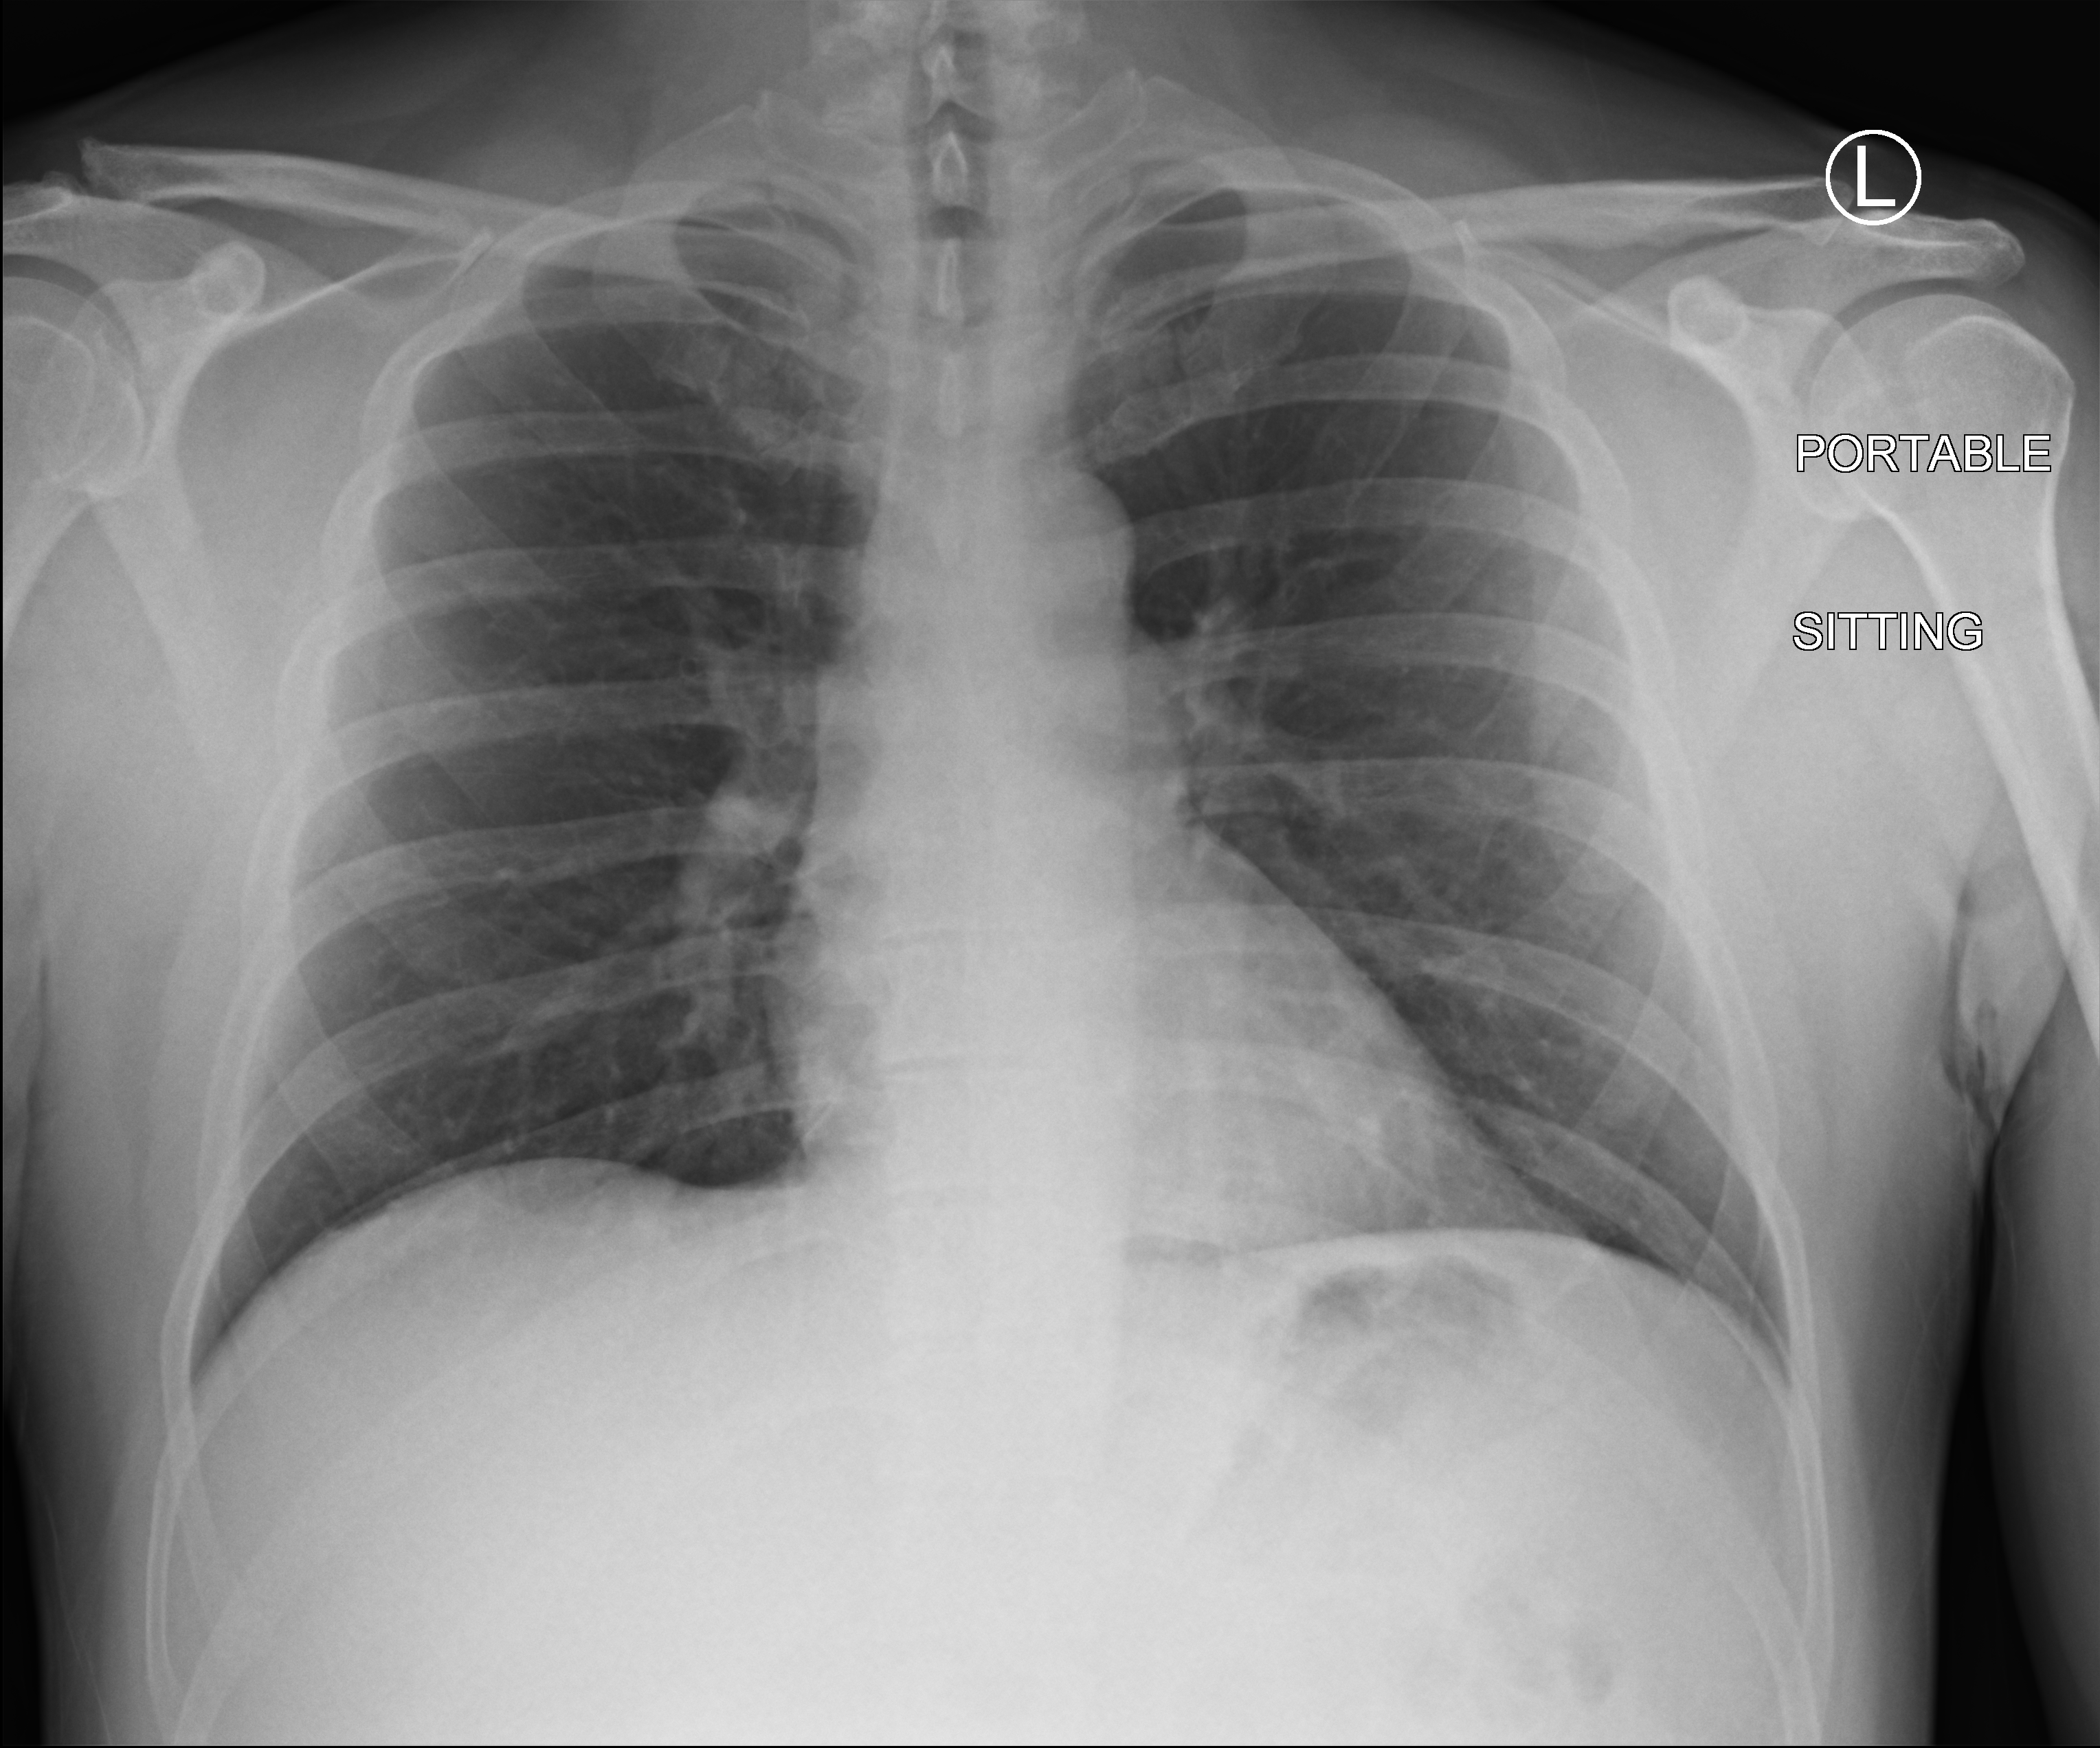
Bedside chest radiograph (computed radiography), anteroposterior (AP) projection. Male patient hospitalised with COVID-19, age 18–59 years.
Hospital-stay facts (about this admission, not read from this image; timing relative to this image not recorded): mechanically ventilated during this hospital stay: no; admitted to intensive care during this hospital stay: no; length of hospital stay: 1 day.